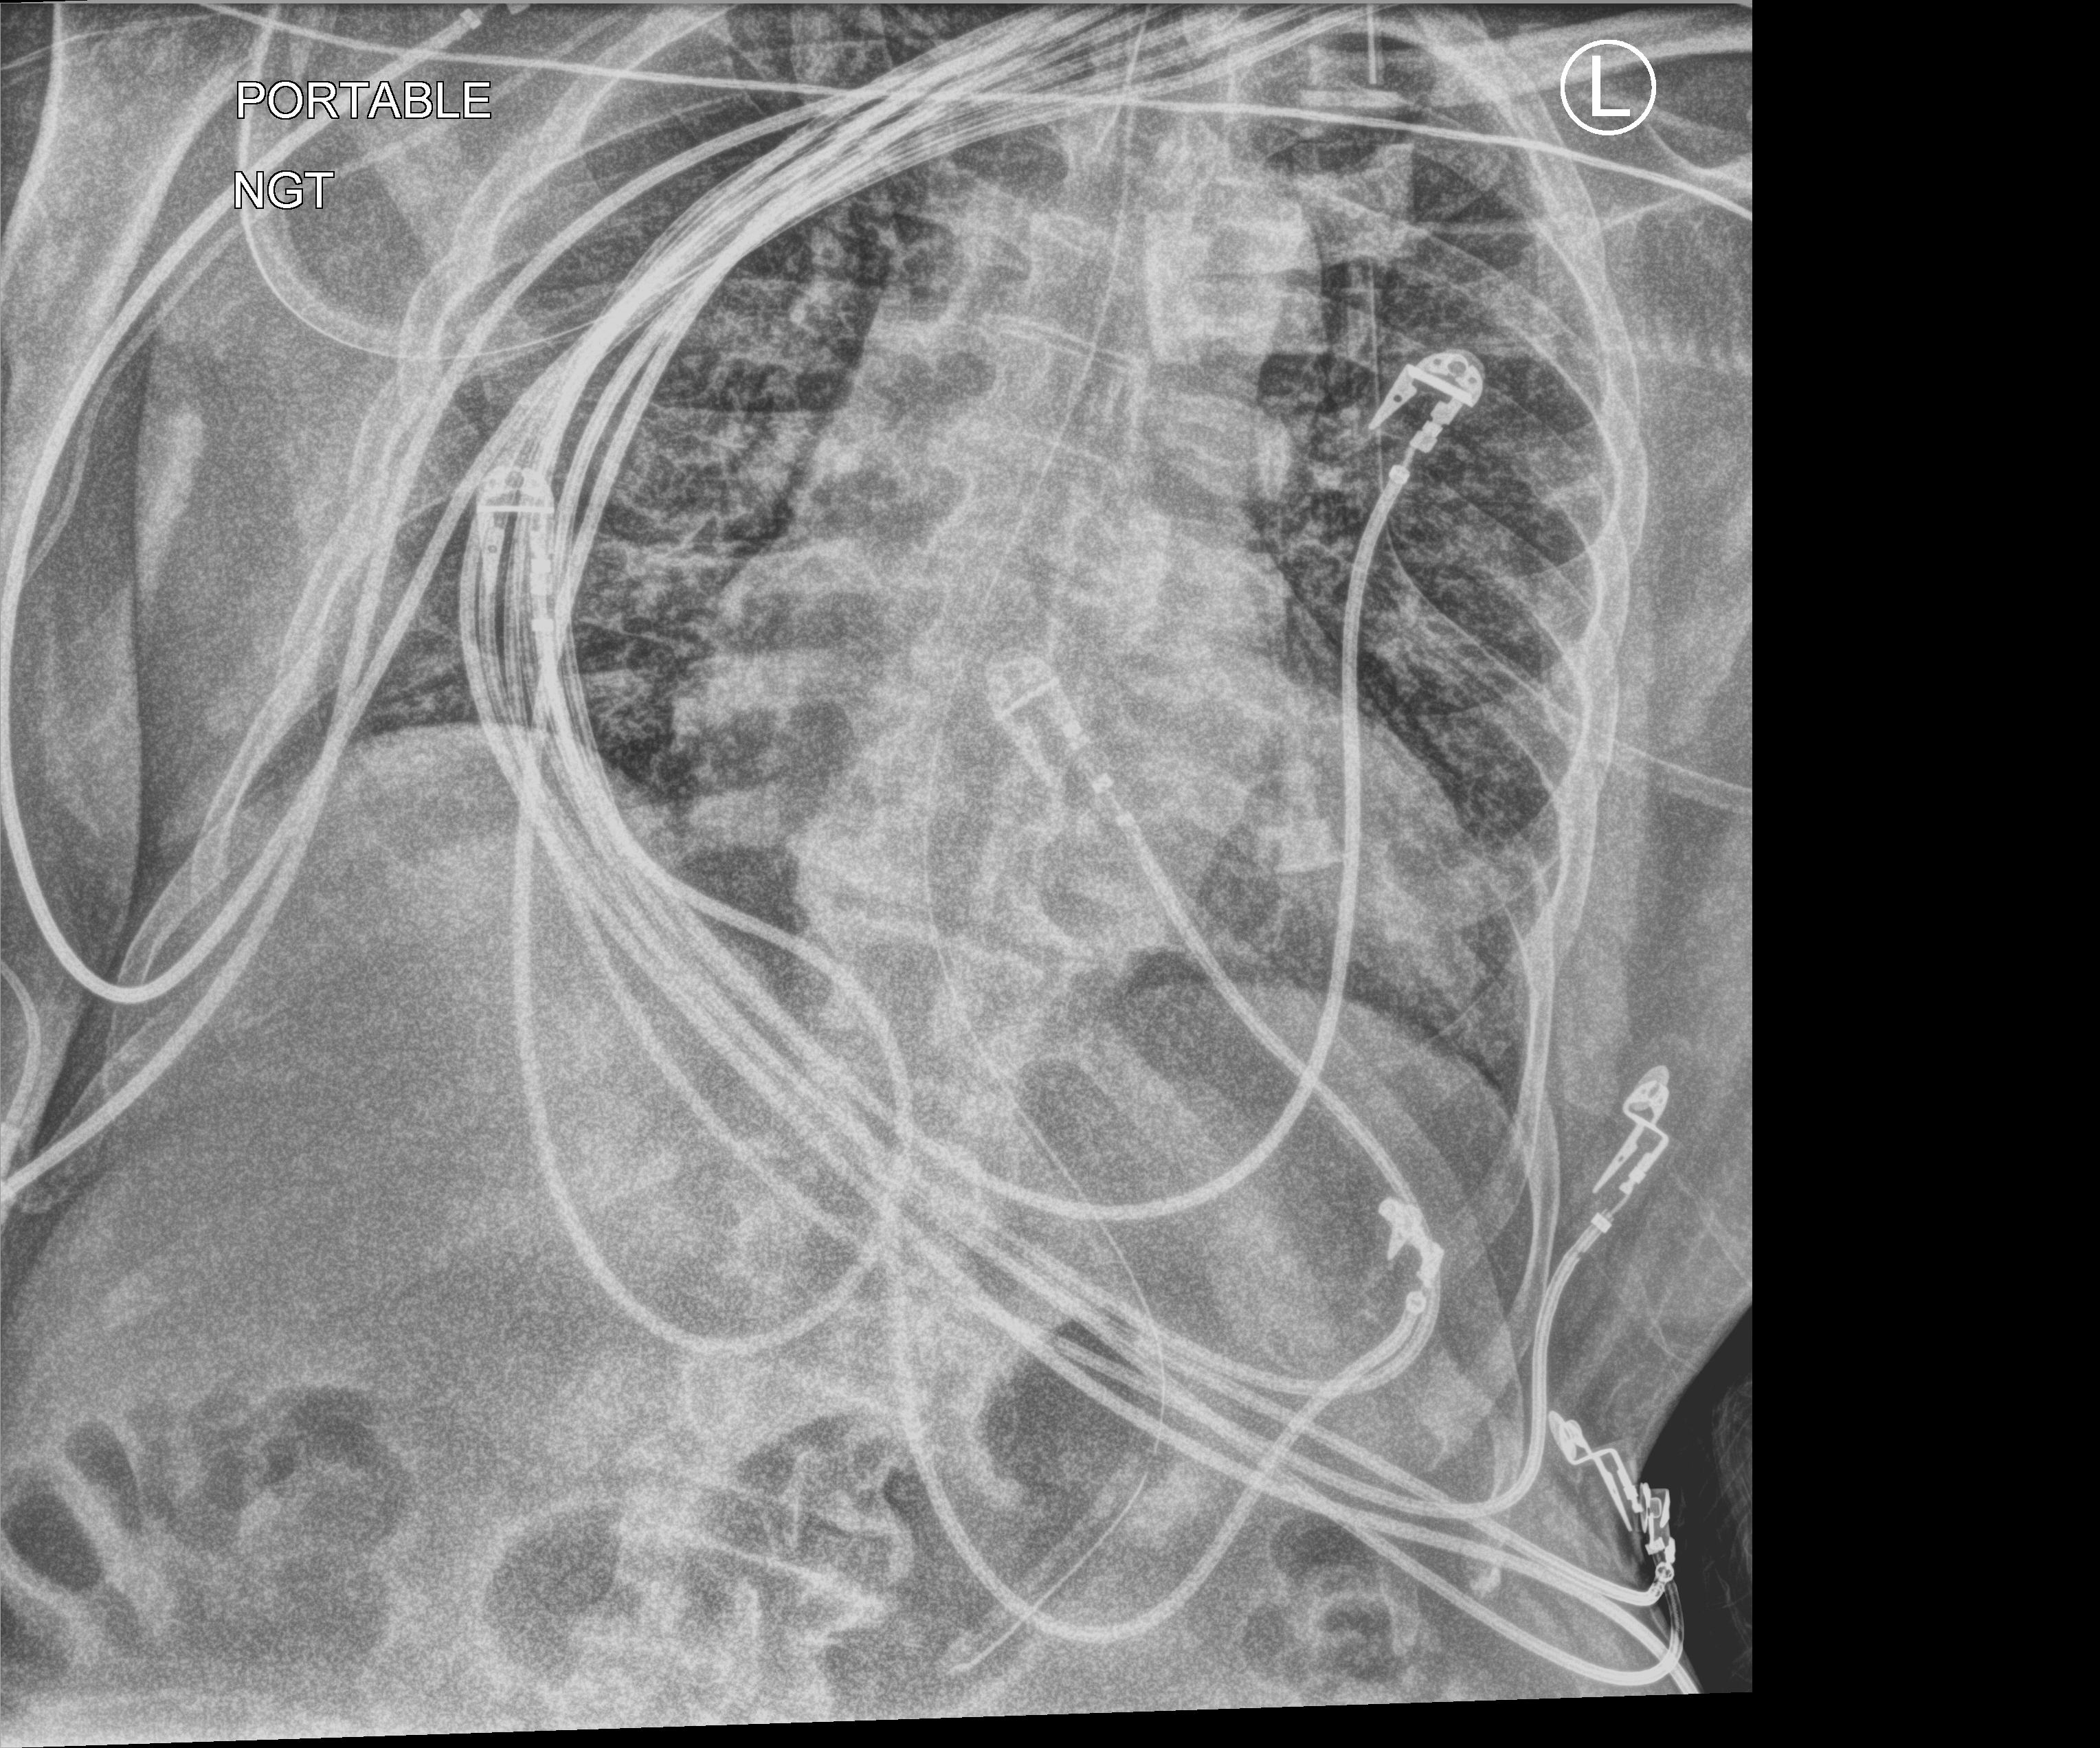
Chest X-ray (portable). Male patient hospitalised with COVID-19, age 60–74 years.
Admission-level facts for this patient (not findings on this image; timing relative to this image not recorded): hypertension (admission record): yes.